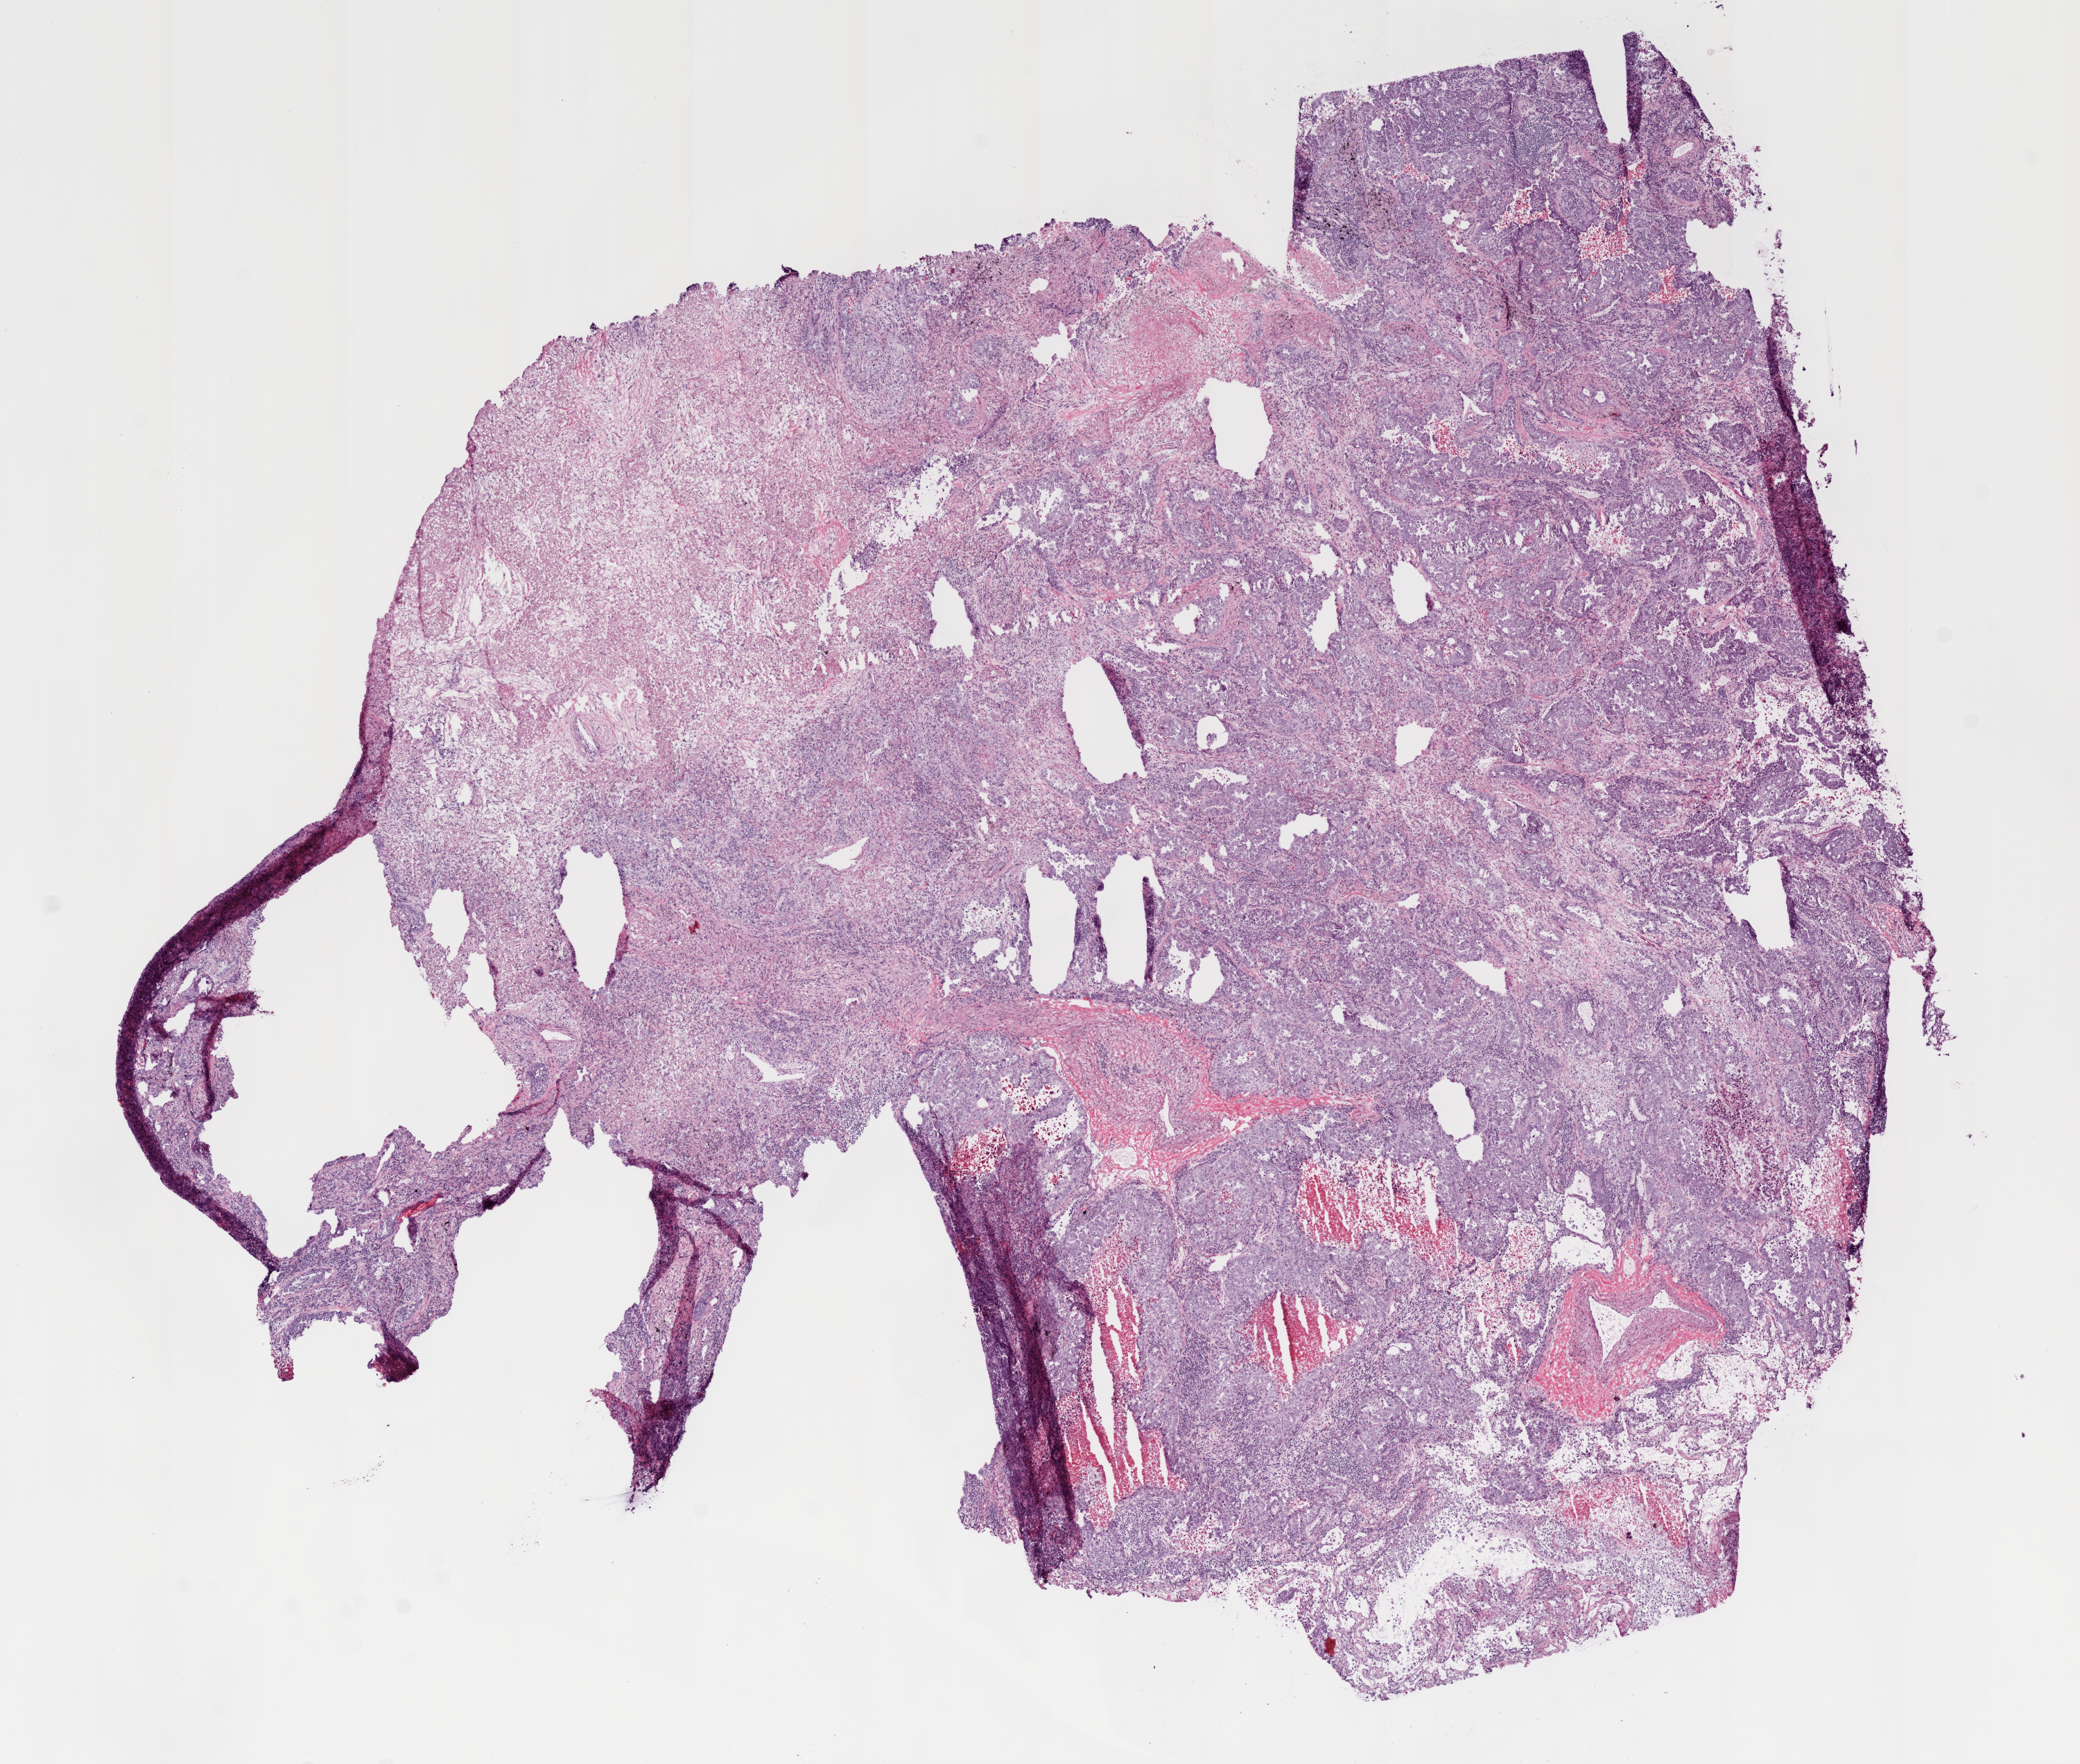
Digitized H&E-stained tissue section (whole slide), whole scanned area (about 12.0 x 10.2 mm, from a 20x scan) shown as a low-resolution overview. Frozen section from the bottom of the tissue portion. Lung, primary tumour sample. Female patient; age at initial diagnosis 77 years. Pathologist review of this section (percent, as recorded): tumour nuclei 75%, normal cells 2%, stromal cells 20%, necrosis 15%.
* AJCC pathologic stage: IA
* TNM: T1 N0 M0
* histologic diagnosis: Adenocarcinoma, NOS (upper lobe, lung)